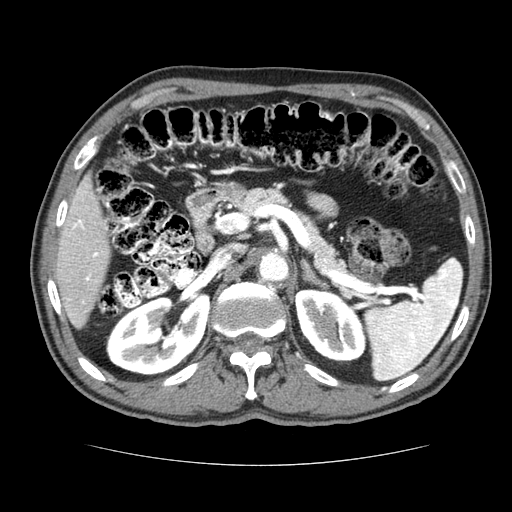
Contrast-enhanced abdominal CT (liver protocol), one axial slice. Slice 37 of 79 in the series (ordered by position). 120 kVp. Soft-tissue window (W 400 / L 40 HU). 512 × 512 image matrix, field of view 360 × 360 mm. Case-level facts recorded for this patient, not image findings: diagnosis: hepatocellular carcinoma (patient treated with transarterial chemoembolisation; whether this scan precedes or follows treatment is not stated here); TNM stage (as recorded): Stage-I; Child-Pugh class: A; tumour nodularity: uninodular.
Annotated regions visible in this slice (semi-automatic segmentation, software-assisted and operator-edited):
- liver parenchyma outside the tumour (the mass and vessels are separate outlines, so this box may not span the whole liver): bounding box (x1, y1, x2, y2) in pixels: (54, 175, 110, 328)
- liver vessels: (68, 219, 99, 303)